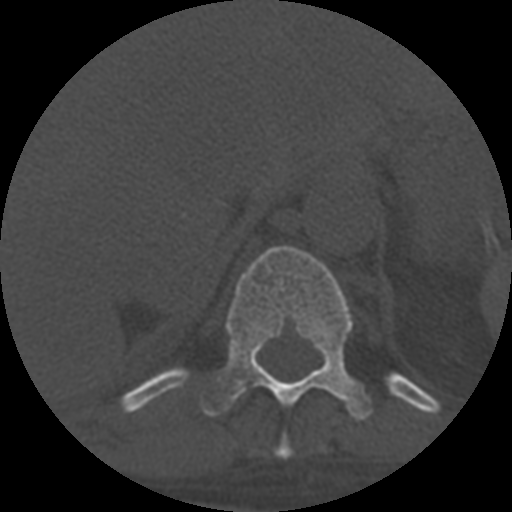
CT including the spine, one axial slice. Position 338 of 708 along the scan axis. Reconstruction kernel STANDARD. One of 3 acquisitions stored at this slice position. Bone window (W 1800 / L 400 HU). 1.25 mm slice thickness. 512 × 512 image matrix. Patient age 55 years. Case-level facts recorded for this patient, not image findings: primary cancer: colon.
Annotated regions visible in this slice (semi-automatically segmented with operator editing):
- T10 vertebra: bounding box (x1, y1, x2, y2) in pixels: (275, 435, 293, 459)
- T11 vertebra: (201, 245, 372, 420)